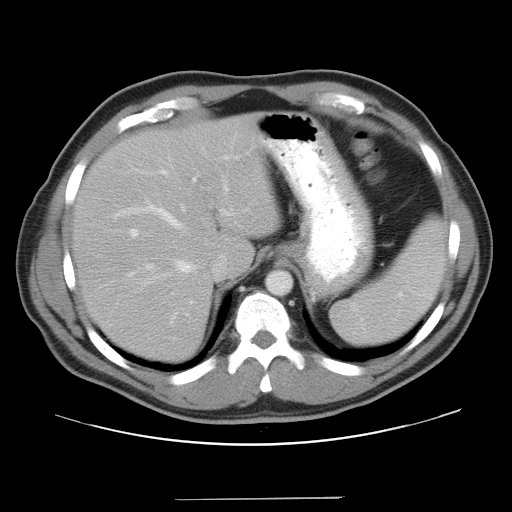
Contrast-enhanced abdominal CT, one axial slice; slice 30 of 37 in the series (ordered by position); reconstruction kernel STANDARD; 120 kVp; soft-tissue window (W 400 / L 40 HU); 7.5 mm slice thickness; 512 × 512 image matrix, field of view 400 × 400 mm. Male patient, age 46 years. Case-level facts recorded for this patient, not image findings: diagnosis: colorectal cancer liver metastases, imaged before liver resection; multiple liver metastases: yes; largest metastasis: 1 cm; disease in both lobes: no.
Outlined on this slice (expert manual segmentation):
- hepatic veins: bounding box [x1, y1, x2, y2] px = [124, 183, 257, 286]
- liver: [77, 118, 275, 359]
- planned liver remnant (the part of the liver to remain after resection): [77, 118, 275, 359]
- portal vein (with intrahepatic branches): [129, 155, 240, 339]
- liver metastasis: [116, 162, 123, 169]